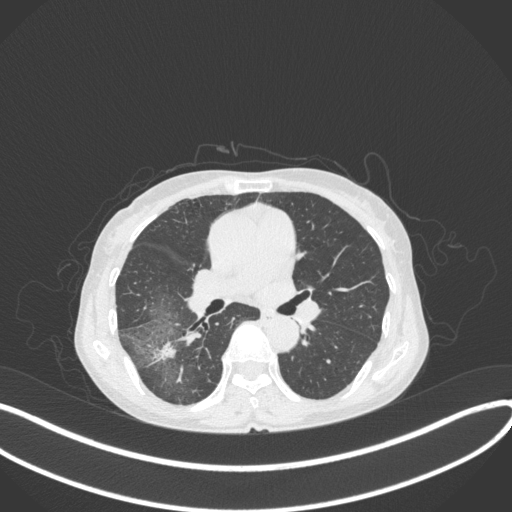
Chest CT, one axial slice. Position 219 of 379 along the scan axis. 120 kVp. Lung window (W 1500 / L -600 HU). 1 mm slice thickness. 512 × 512 image matrix, field of view 400 × 400 mm. Patient: female, 69 years. From the clinical record (not read from this slice): clinical TNM (as recorded): T1b N0 M0; histopathological grade: G2-3.
Outlined on this slice (bounding box drawn by a radiologist):
- lung tumour (recorded histology: adenocarcinoma): bounding box (x1, y1, x2, y2) in pixels: (151, 339, 181, 369)